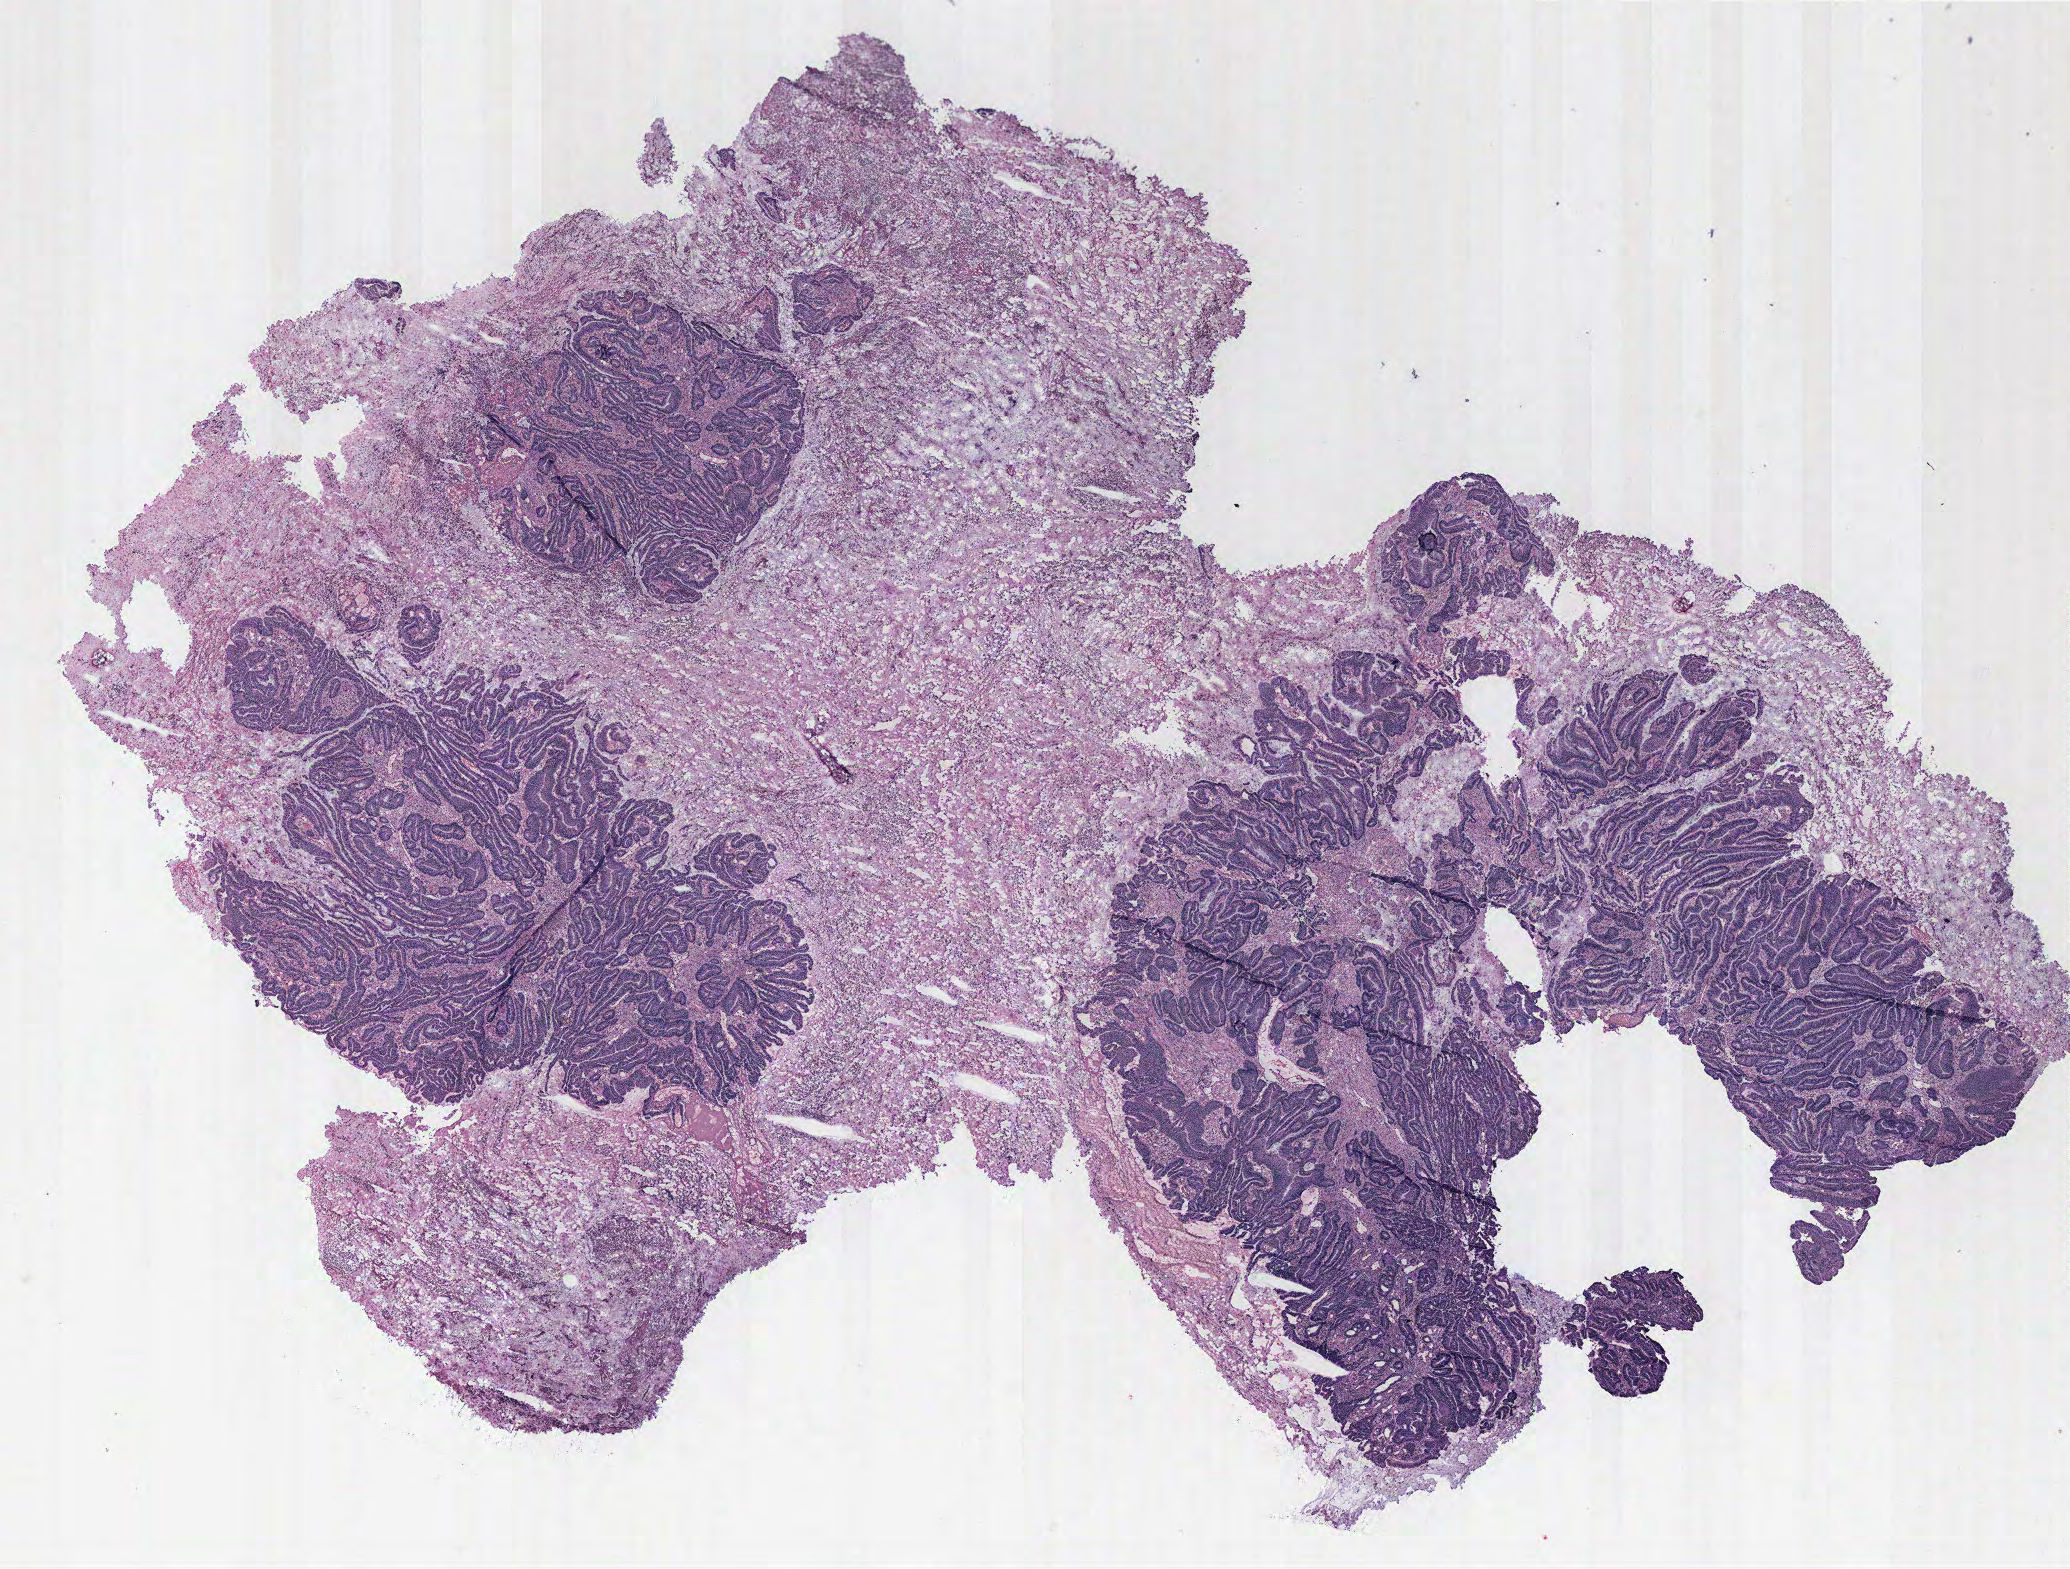
Whole-slide histology image, Hematoxylin and eosin (H&E) stained — whole scanned area (about 16.6 x 12.6 mm, slide scanned at 40x) shown as a low-resolution overview; normal (non-tumour) tissue sample, colon. Patient: female, age 76 years.
This section: normal (non-tumour) tissue from the same patient. Patient diagnosis: Adenocarcinoma, NOS.